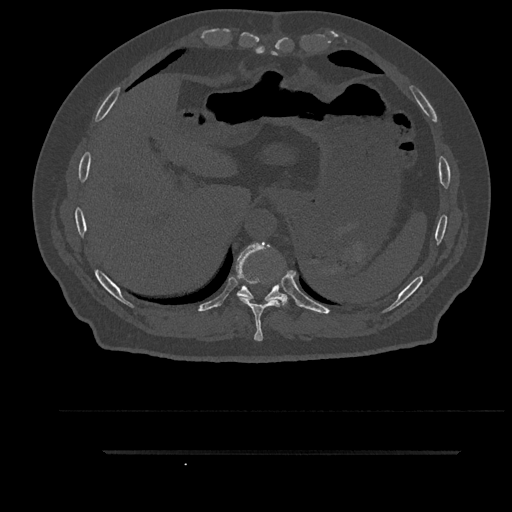
CT including the spine, one axial slice. Slice 396 of 797 in the series (ordered by position). Reconstruction kernel Br40s/3. 120 kVp. Bone window (W 1800 / L 400 HU). 512 × 512 image matrix, field of view 432 × 432 mm. Patient: male, 63 years. Case-level facts recorded for this patient, not image findings: primary cancer: renal.
Outlined on this slice (semi-automatically segmented with operator editing):
- T10 vertebra: box from (x=236, y=247) to (x=288, y=306) px
- T9 vertebra: (x=236, y=242)–(x=289, y=341)